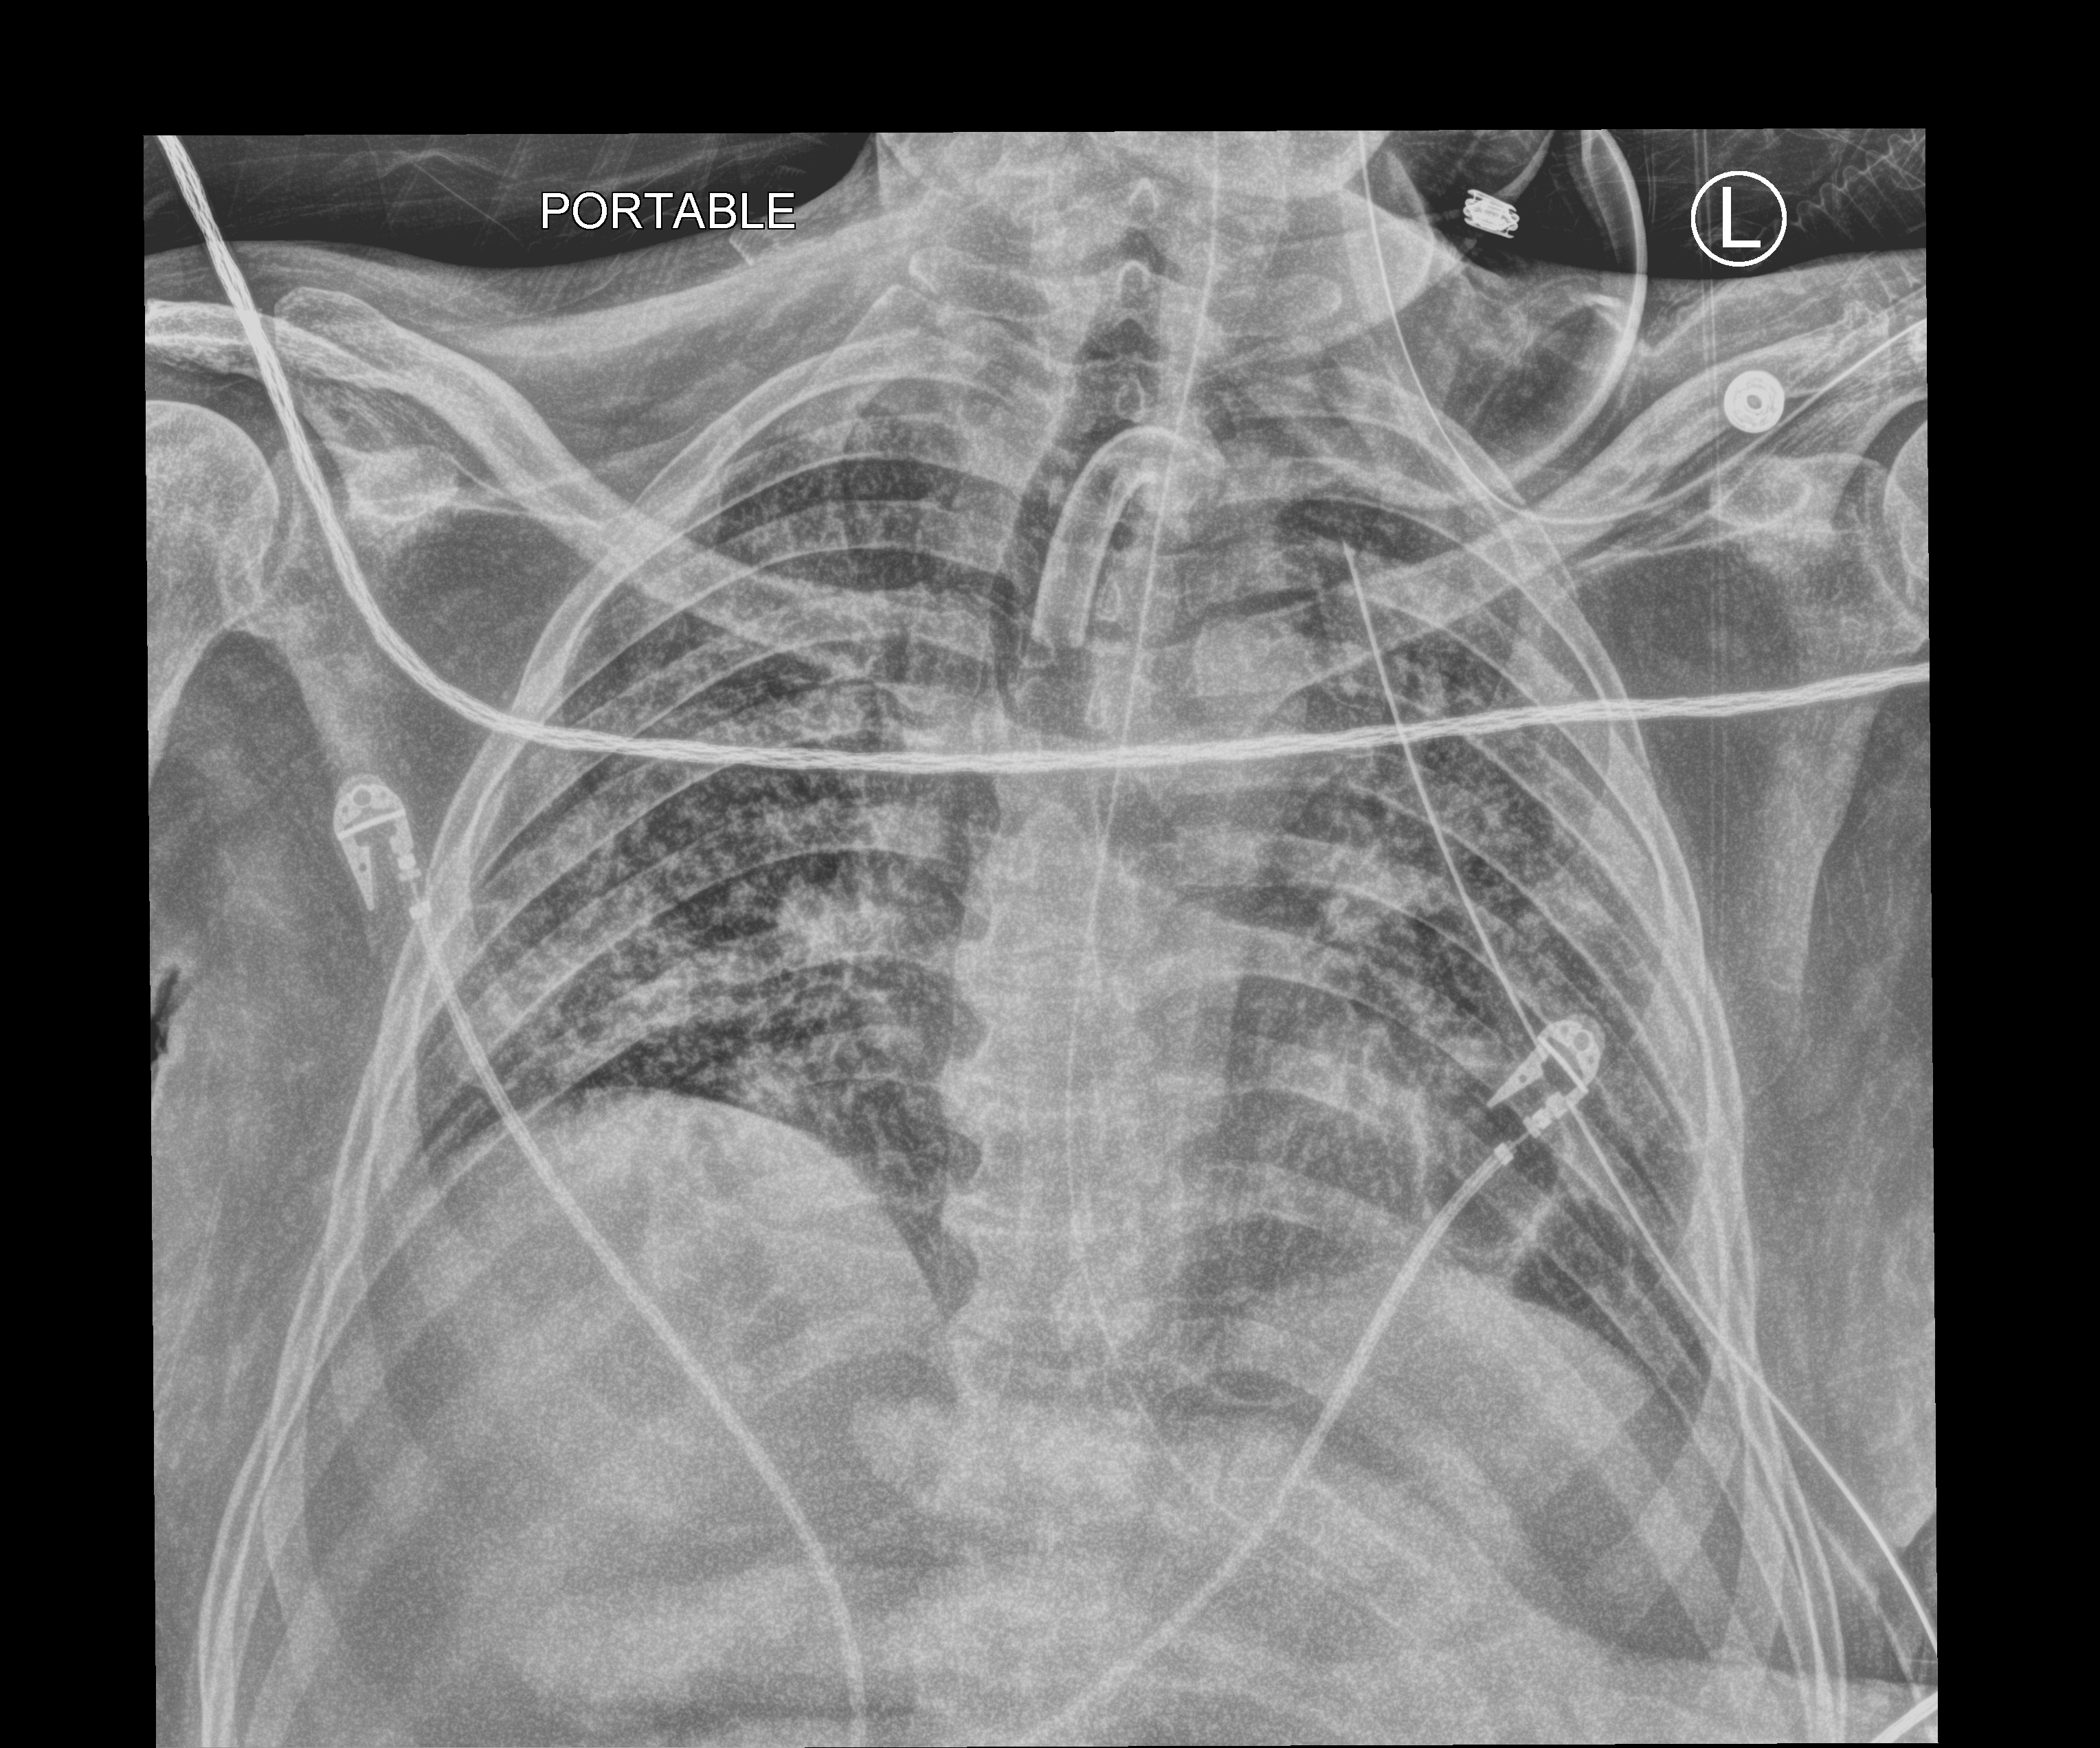
Bedside chest radiograph (computed radiography), anteroposterior (AP) projection. Patient hospitalised with COVID-19; male, aged 18–59 years.
Hospital-stay facts (about this admission, not read from this image; timing relative to this image not recorded): admitted to intensive care during this hospital stay: yes.